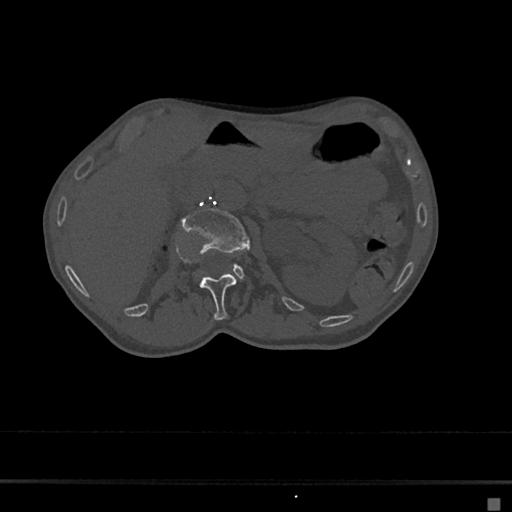
CT including the spine, one axial slice; position 52 of 797 along the scan axis; bone window (W 1800 / L 400 HU); 512 × 512 image matrix, field of view 360 × 360 mm. Patient: female, 68 years. From the clinical record (not read from this slice): primary cancer: renal.
Outlined on this slice (semi-automatic segmentation, software-assisted and operator-edited):
- L1 vertebra: bounding box (x1, y1, x2, y2) in pixels: (199, 273, 236, 321)
- L2 vertebra: (182, 207, 250, 277)